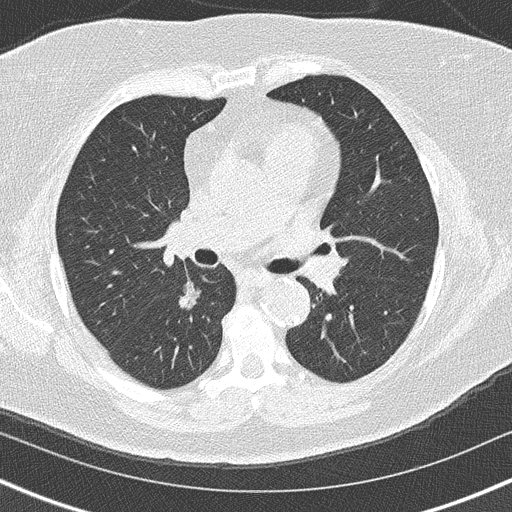
Chest CT (low-dose screening protocol), one axial image; second screening round (one year after baseline); lung window (W 1500 / L -600 HU); 2 mm slice thickness; 120 kVp; slice 61 of 152 in the series; 512 × 512 image matrix. Female participant, aged 60 years at enrolment.
Lesion marked by an expert reader, bounding box [x1, y1, x2, y2] px = [149, 268, 216, 325]. Reader record for this screening exam (exam-level; its link to the box is not recorded): non-calcified nodule or mass ≥4 mm, right lower lobe, 20 × 19 mm, soft tissue attenuation, pre-existing on the prior screen: yes; interval growth: yes. Later outcome: lung cancer diagnosed 139 days after this screen — bronchiolo-alveolar carcinoma, non-mucinous, right lower lobe, stage IA (AJCC 6th edition), 15 mm at pathology.